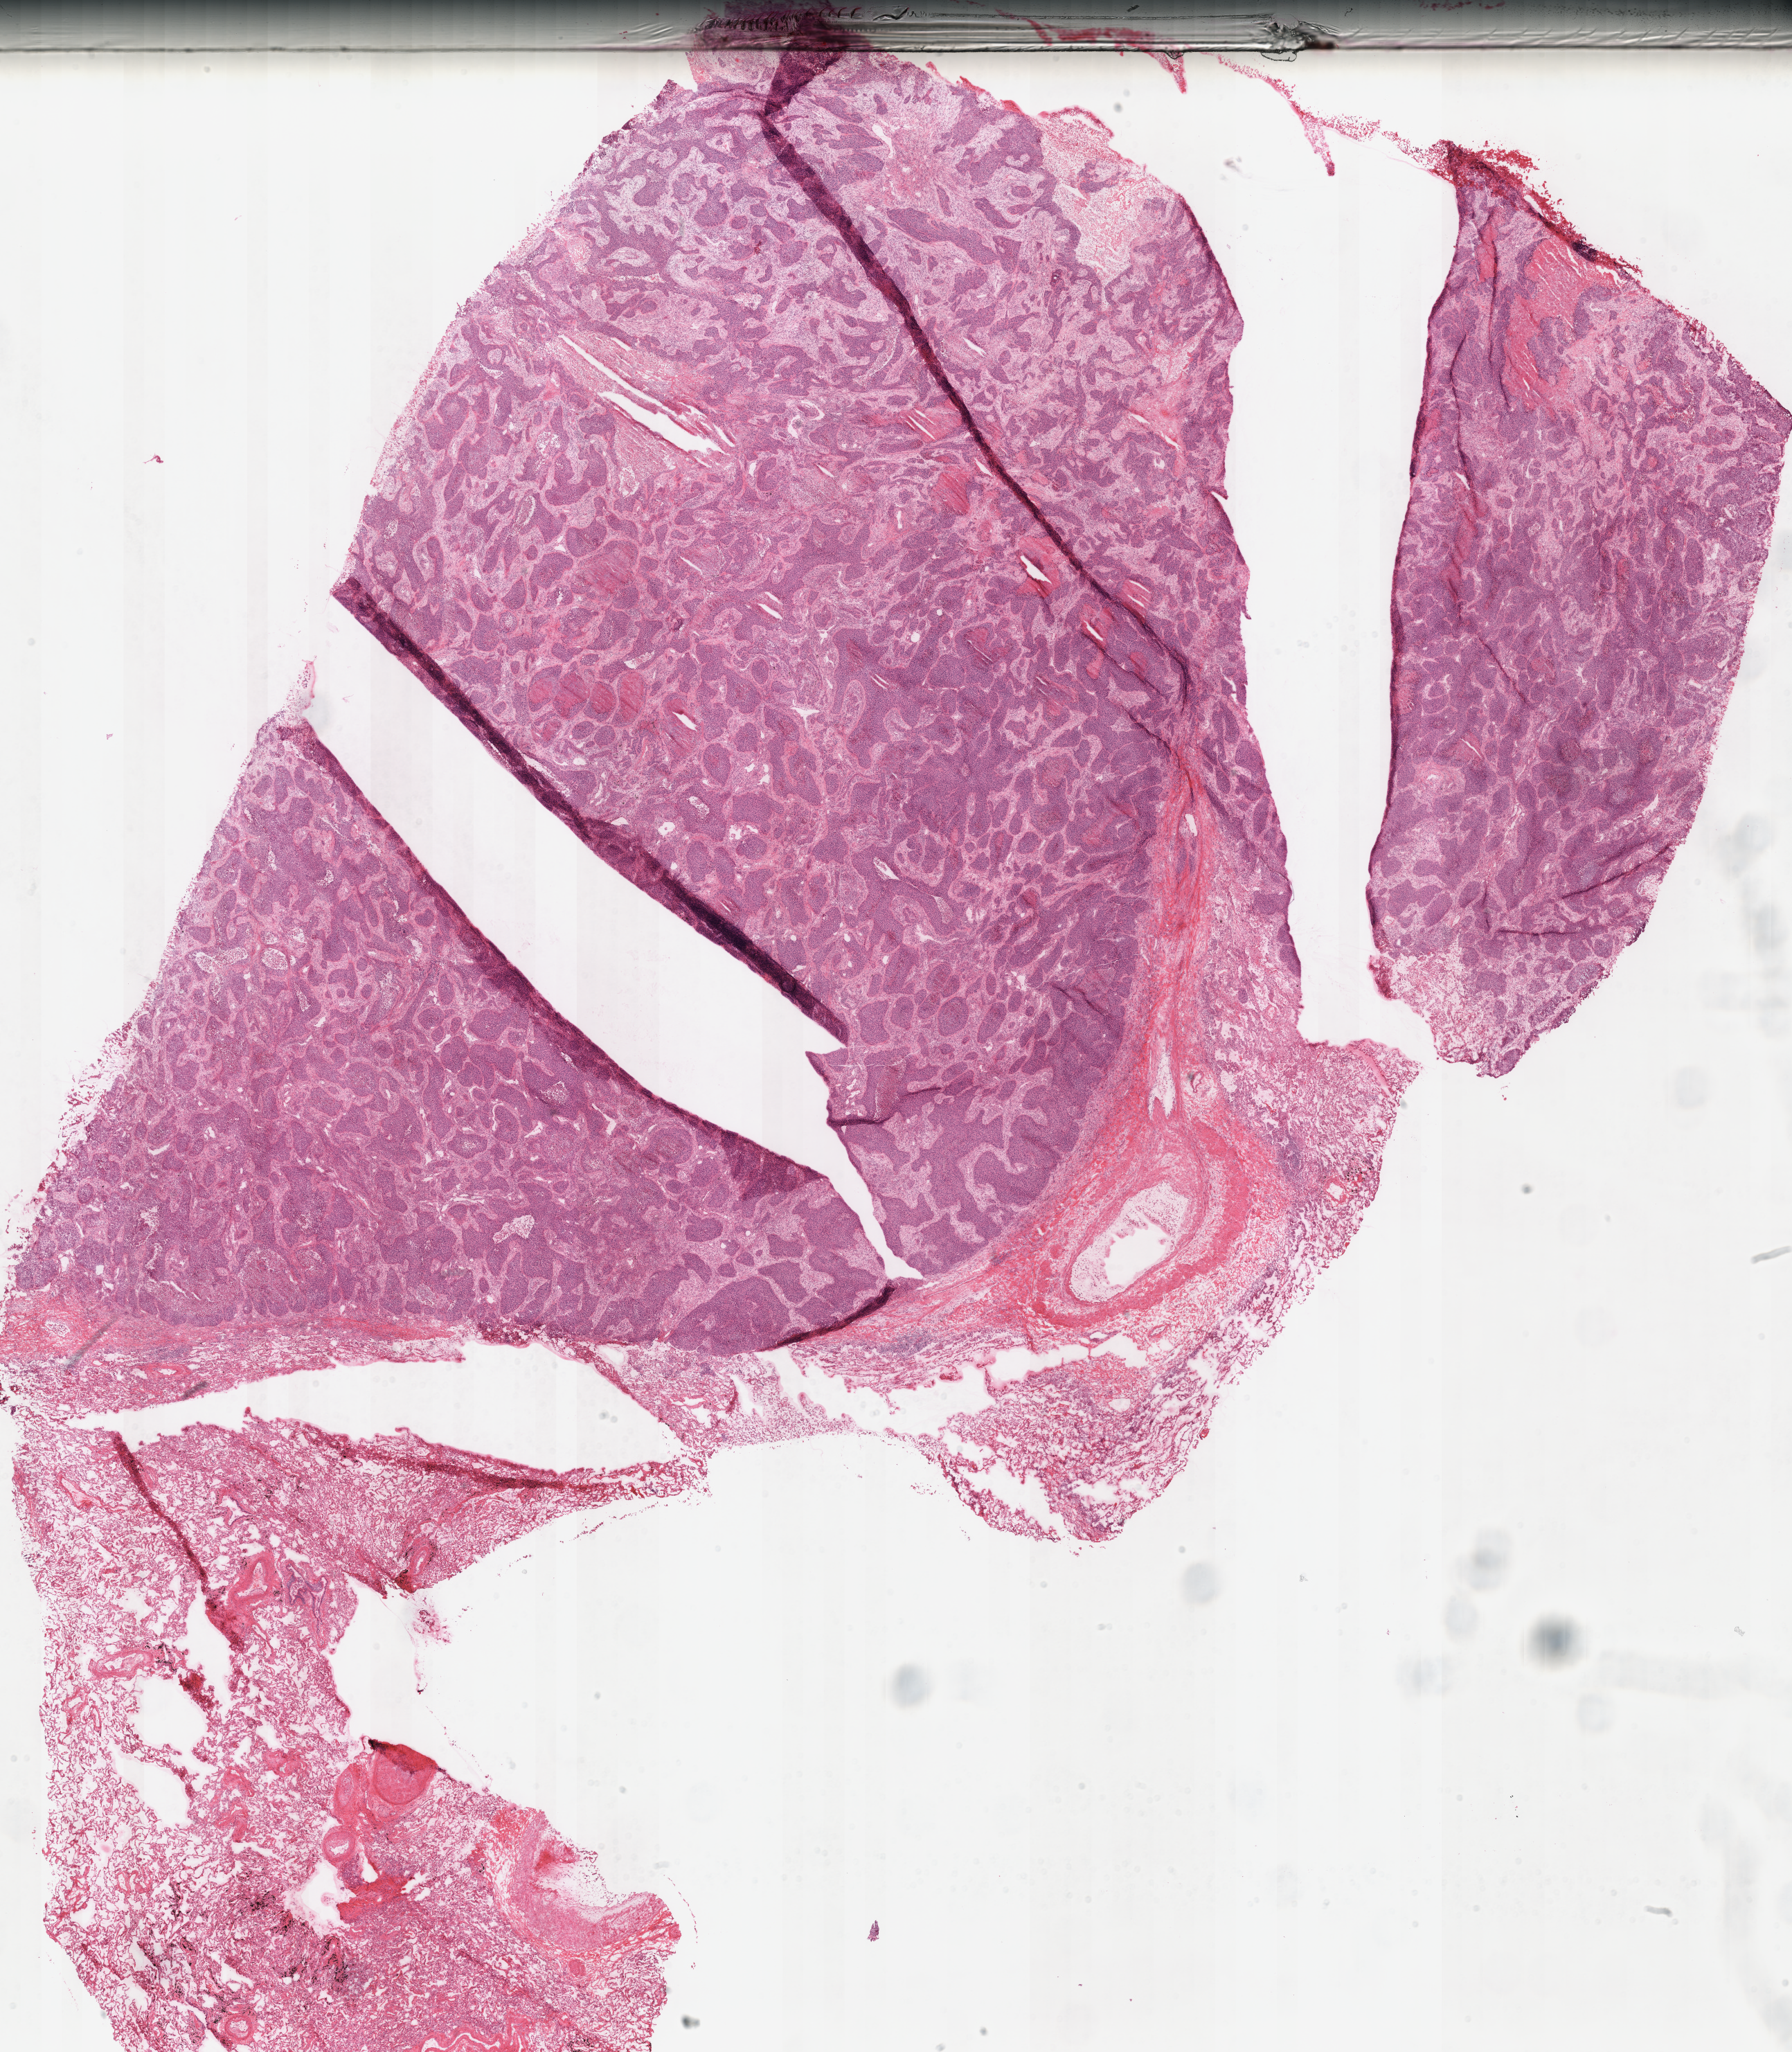
H&E whole-slide image — whole scanned area (about 20.4 x 23.3 mm, slide scanned at 40x) shown as a low-resolution overview, frozen section from the top of the tissue portion, primary tumour sample from the lung. Male, age 73 years at initial diagnosis. Slide review estimates, as recorded: tumour cells 80%, tumour nuclei 80%, normal cells 20%, stromal cells 0%, necrosis 0%. Infiltration values recorded for this section: lymphocyte infiltration 10%, monocyte infiltration 0%, neutrophil infiltration 2%.
Diagnosis: Squamous cell carcinoma, NOS (upper lobe, lung). Laterality: right. AJCC pathologic stage: IIB (7th edition). TNM: T2b N1 M0.